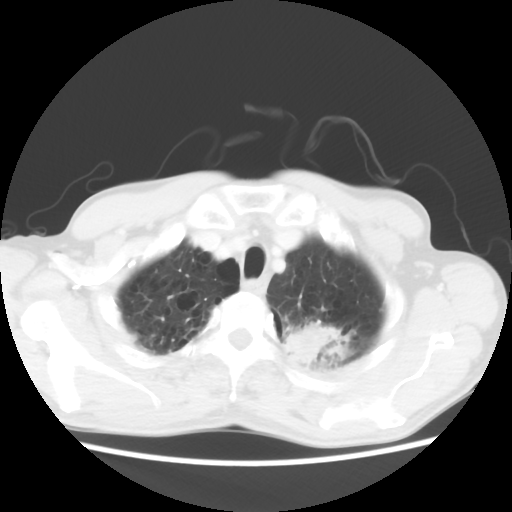
Chest CT, one axial slice; position 56 of 64 along the scan axis; reconstruction kernel STANDARD; 120 kVp; lung window (W 1500 / L -600 HU); 512 × 512 image matrix, field of view 346 × 346 mm. Male patient, age 63 years. Case-level facts recorded for this patient, not image findings: clinical TNM (as recorded): T2 N0 M0.
Outlined on this slice (rectangle marked by the reading radiologist):
- lung tumour (recorded histology: adenocarcinoma): box from (x=281, y=315) to (x=346, y=382) px